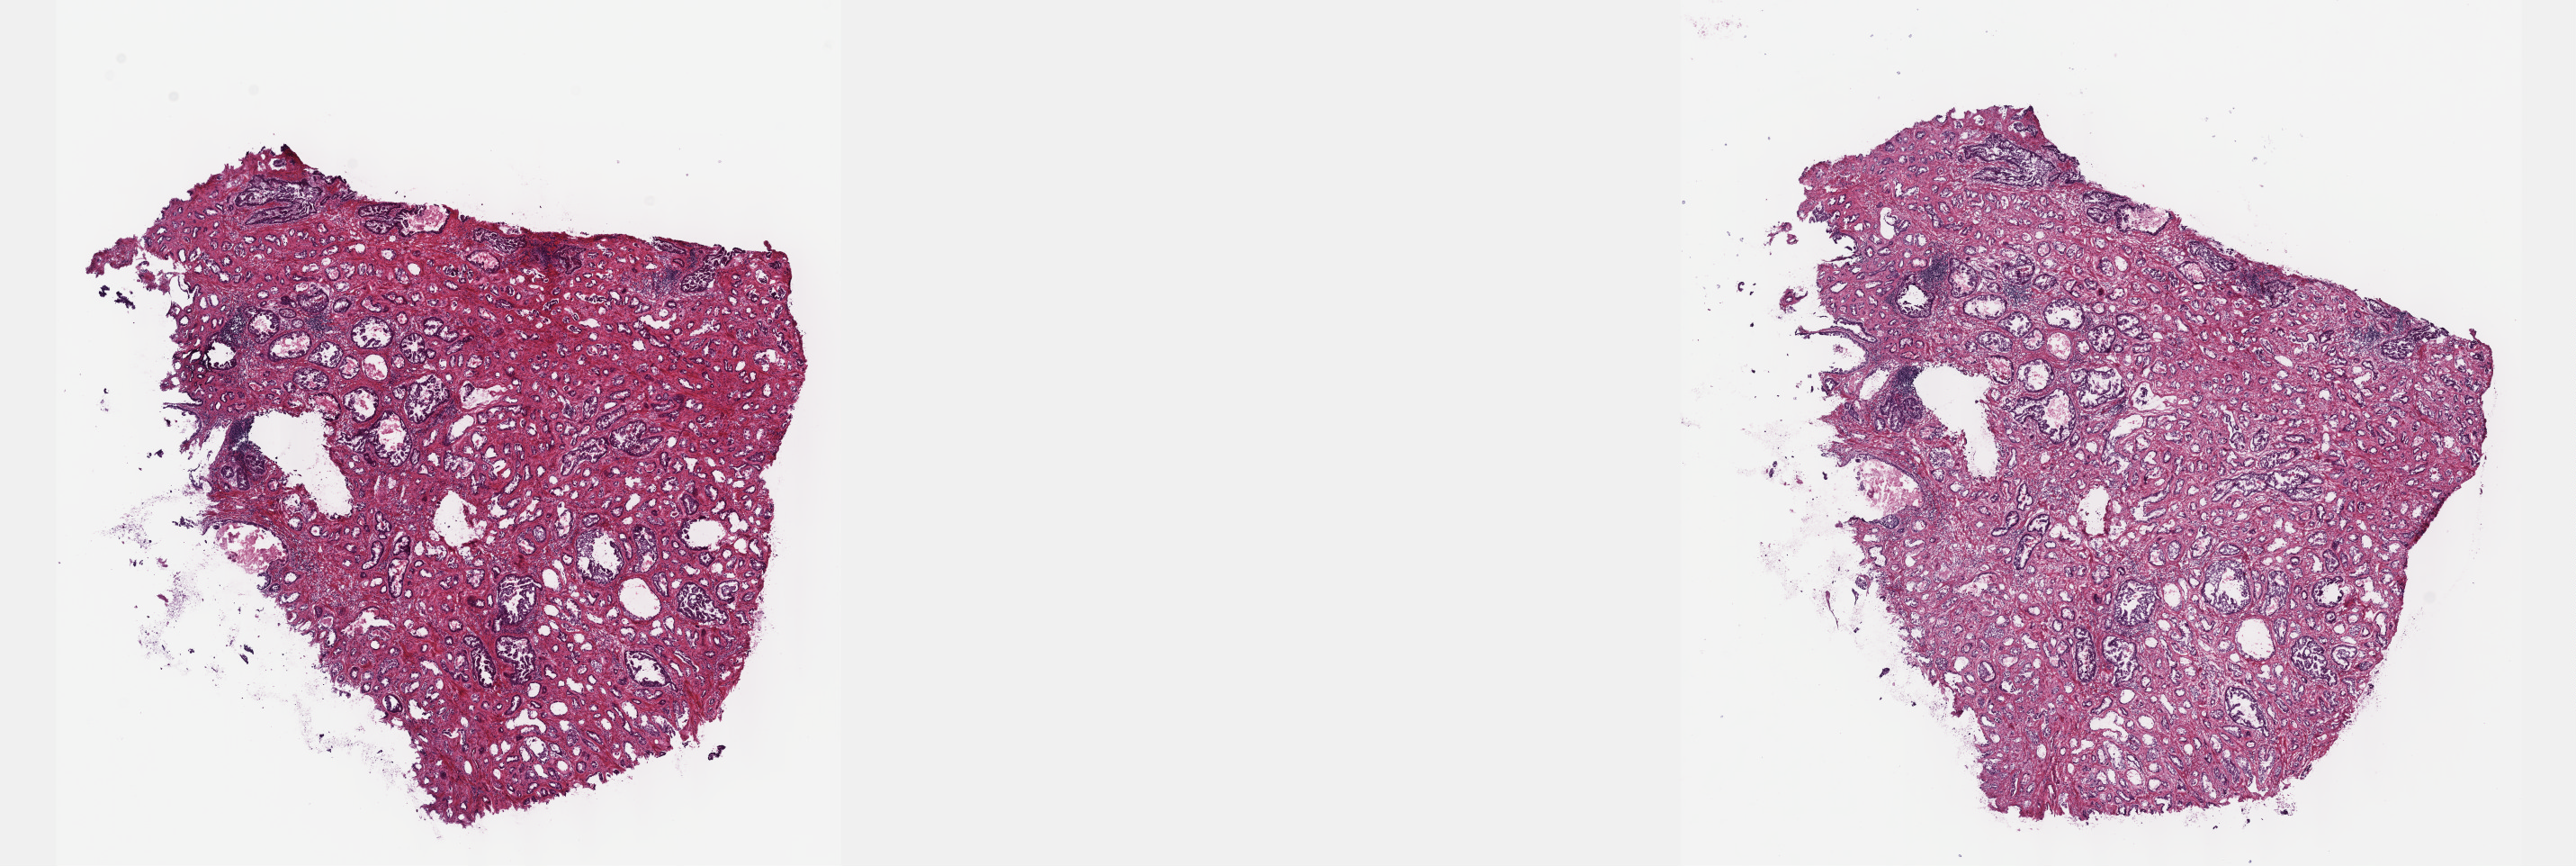
H&E-stained whole-slide image — low-resolution overview of the scanned area, about 23.1 x 7.8 mm. Frozen section from the top of the tissue portion. Primary tumour sample from the prostate. Male, age 60 years at initial diagnosis. Gleason score: 8 (5+3). Slide review estimates, as recorded: tumour cells 60%, tumour nuclei 70%, normal cells 30%, stromal cells 10%, necrosis 0%. Infiltration values recorded for this section: lymphocyte infiltration 0%, monocyte infiltration 0%, neutrophil infiltration 0%.
Laterality: bilateral. Lymph nodes positive (case pathology): 0 of 12 examined. Pathologic diagnosis: Infiltrating duct carcinoma, NOS (prostate gland).